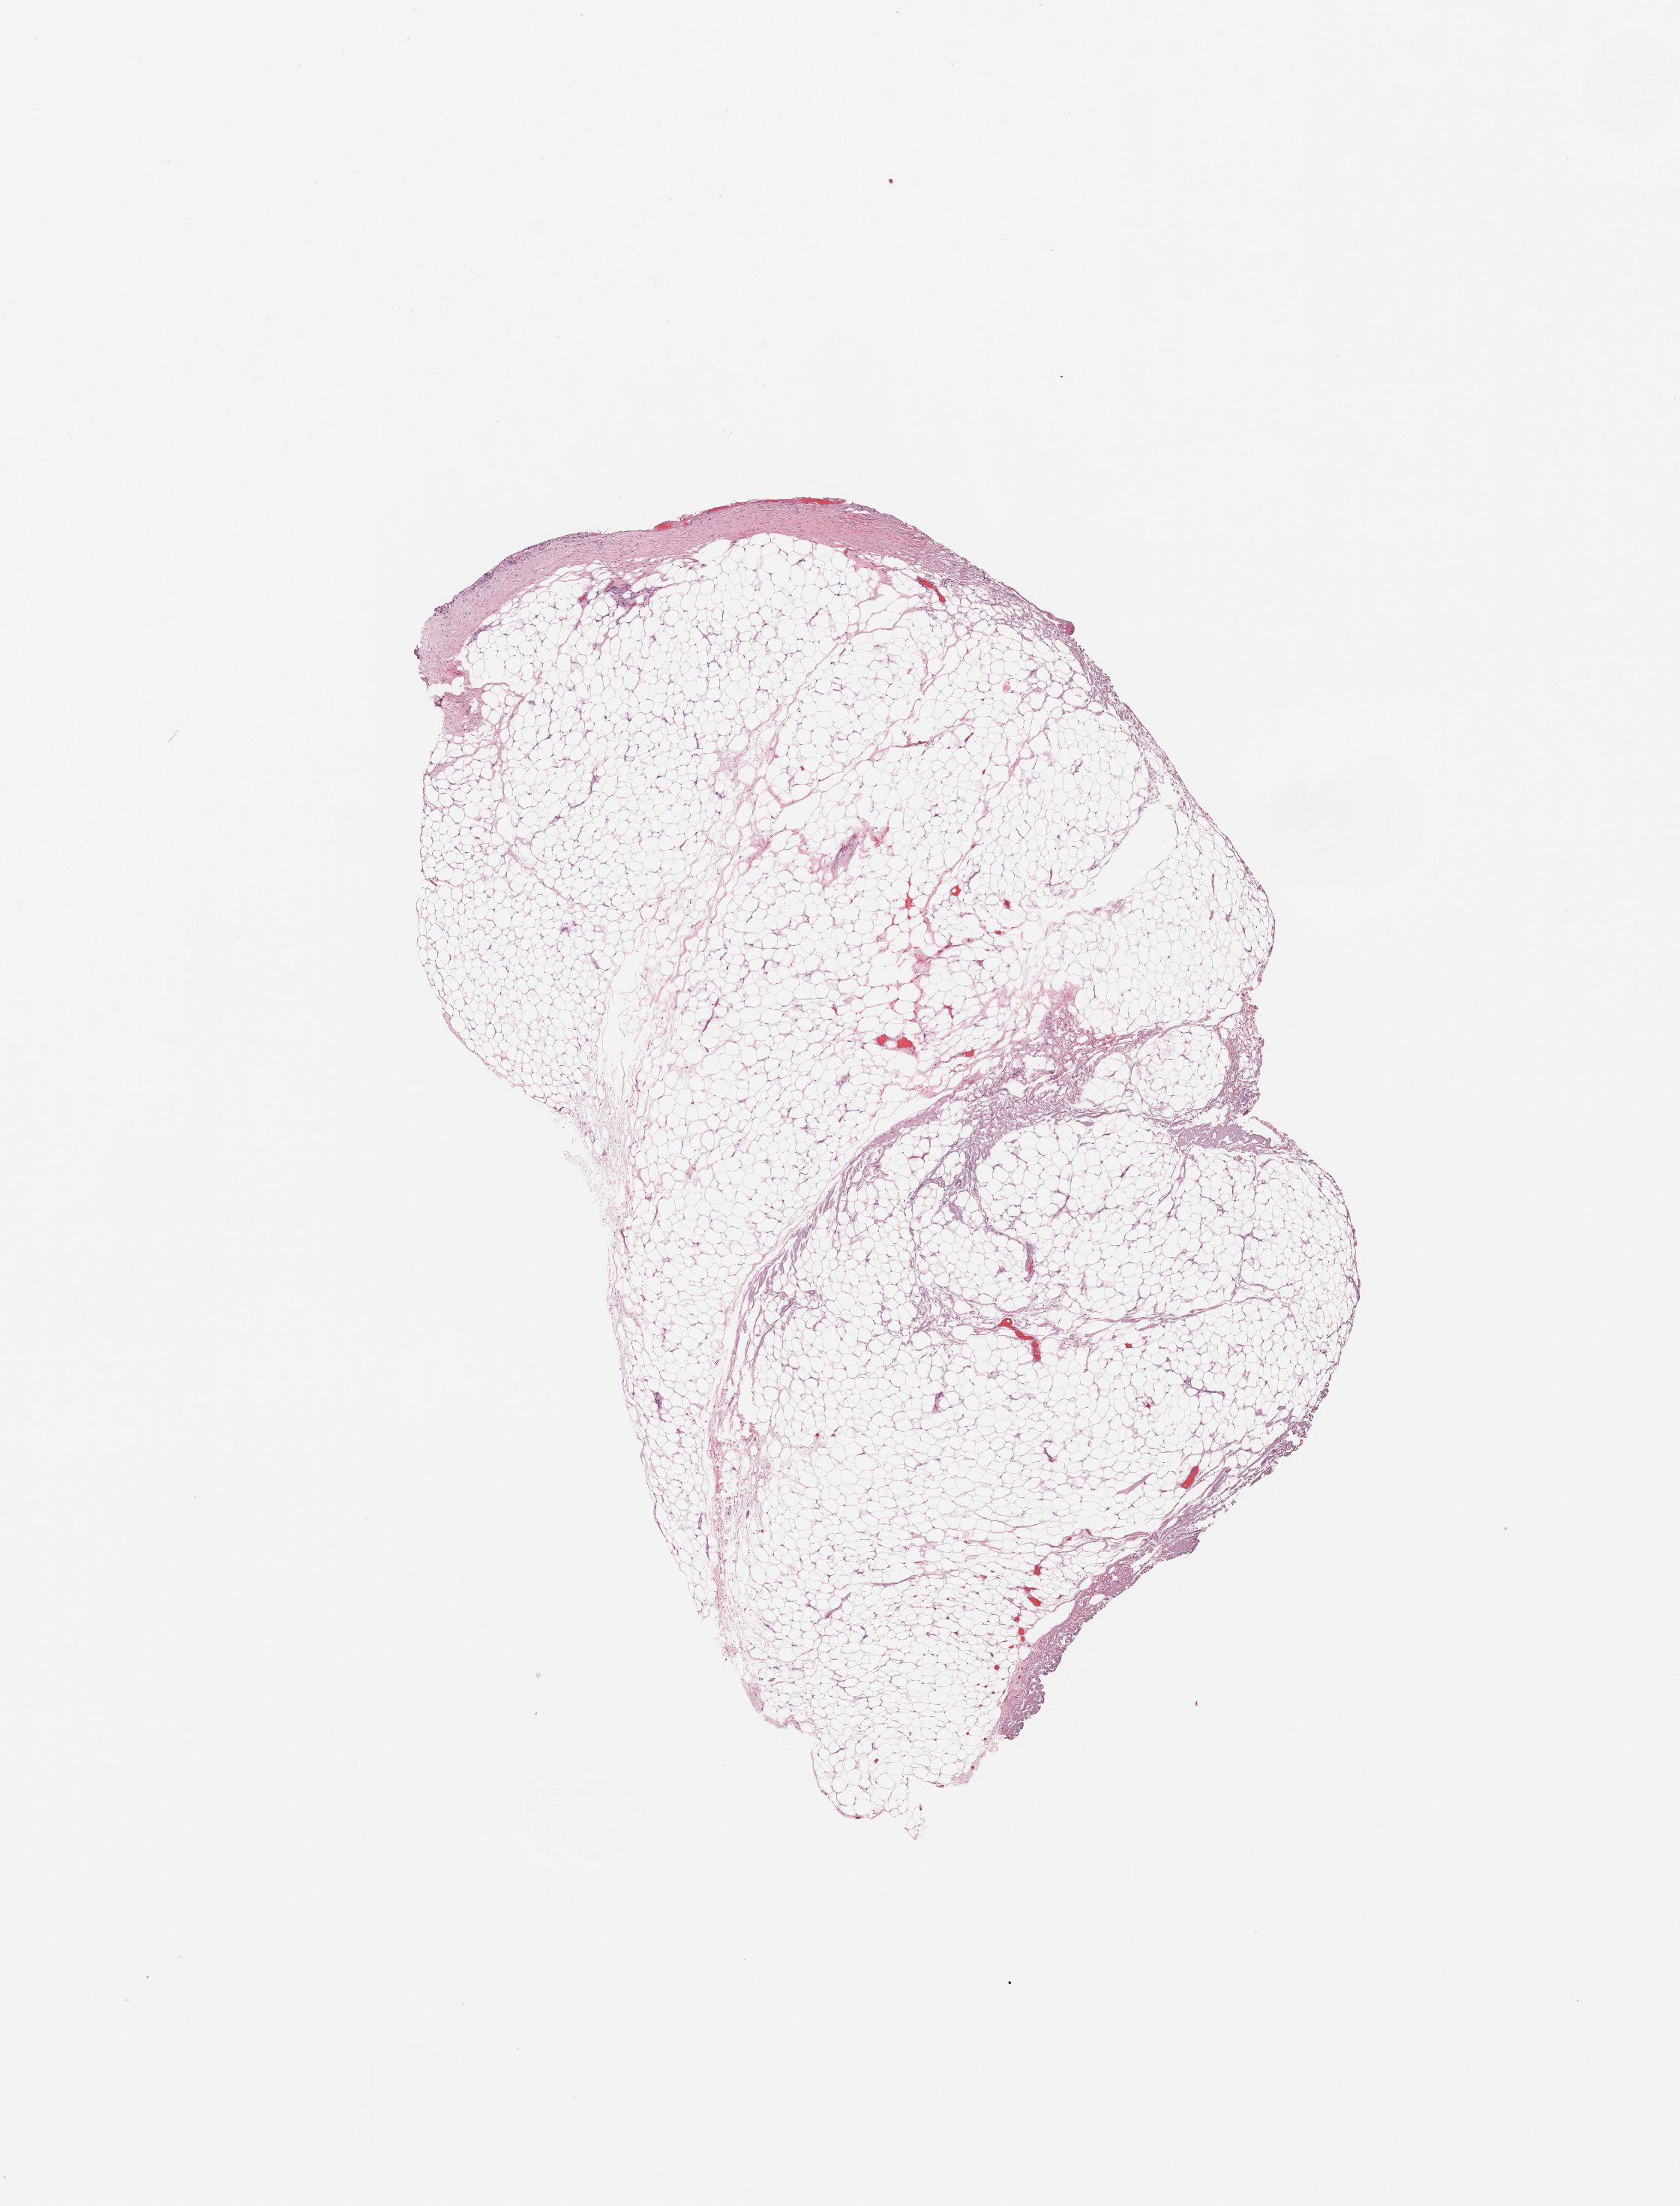
Whole-slide histology image, H&E, low-resolution overview of the scanned area, about 8.9 x 11.6 mm; kidney, normal (non-tumour) tissue. 74-year-old male patient.
This section: normal (non-tumour) tissue from the same patient. Patient diagnosis: Renal cell carcinoma, NOS.